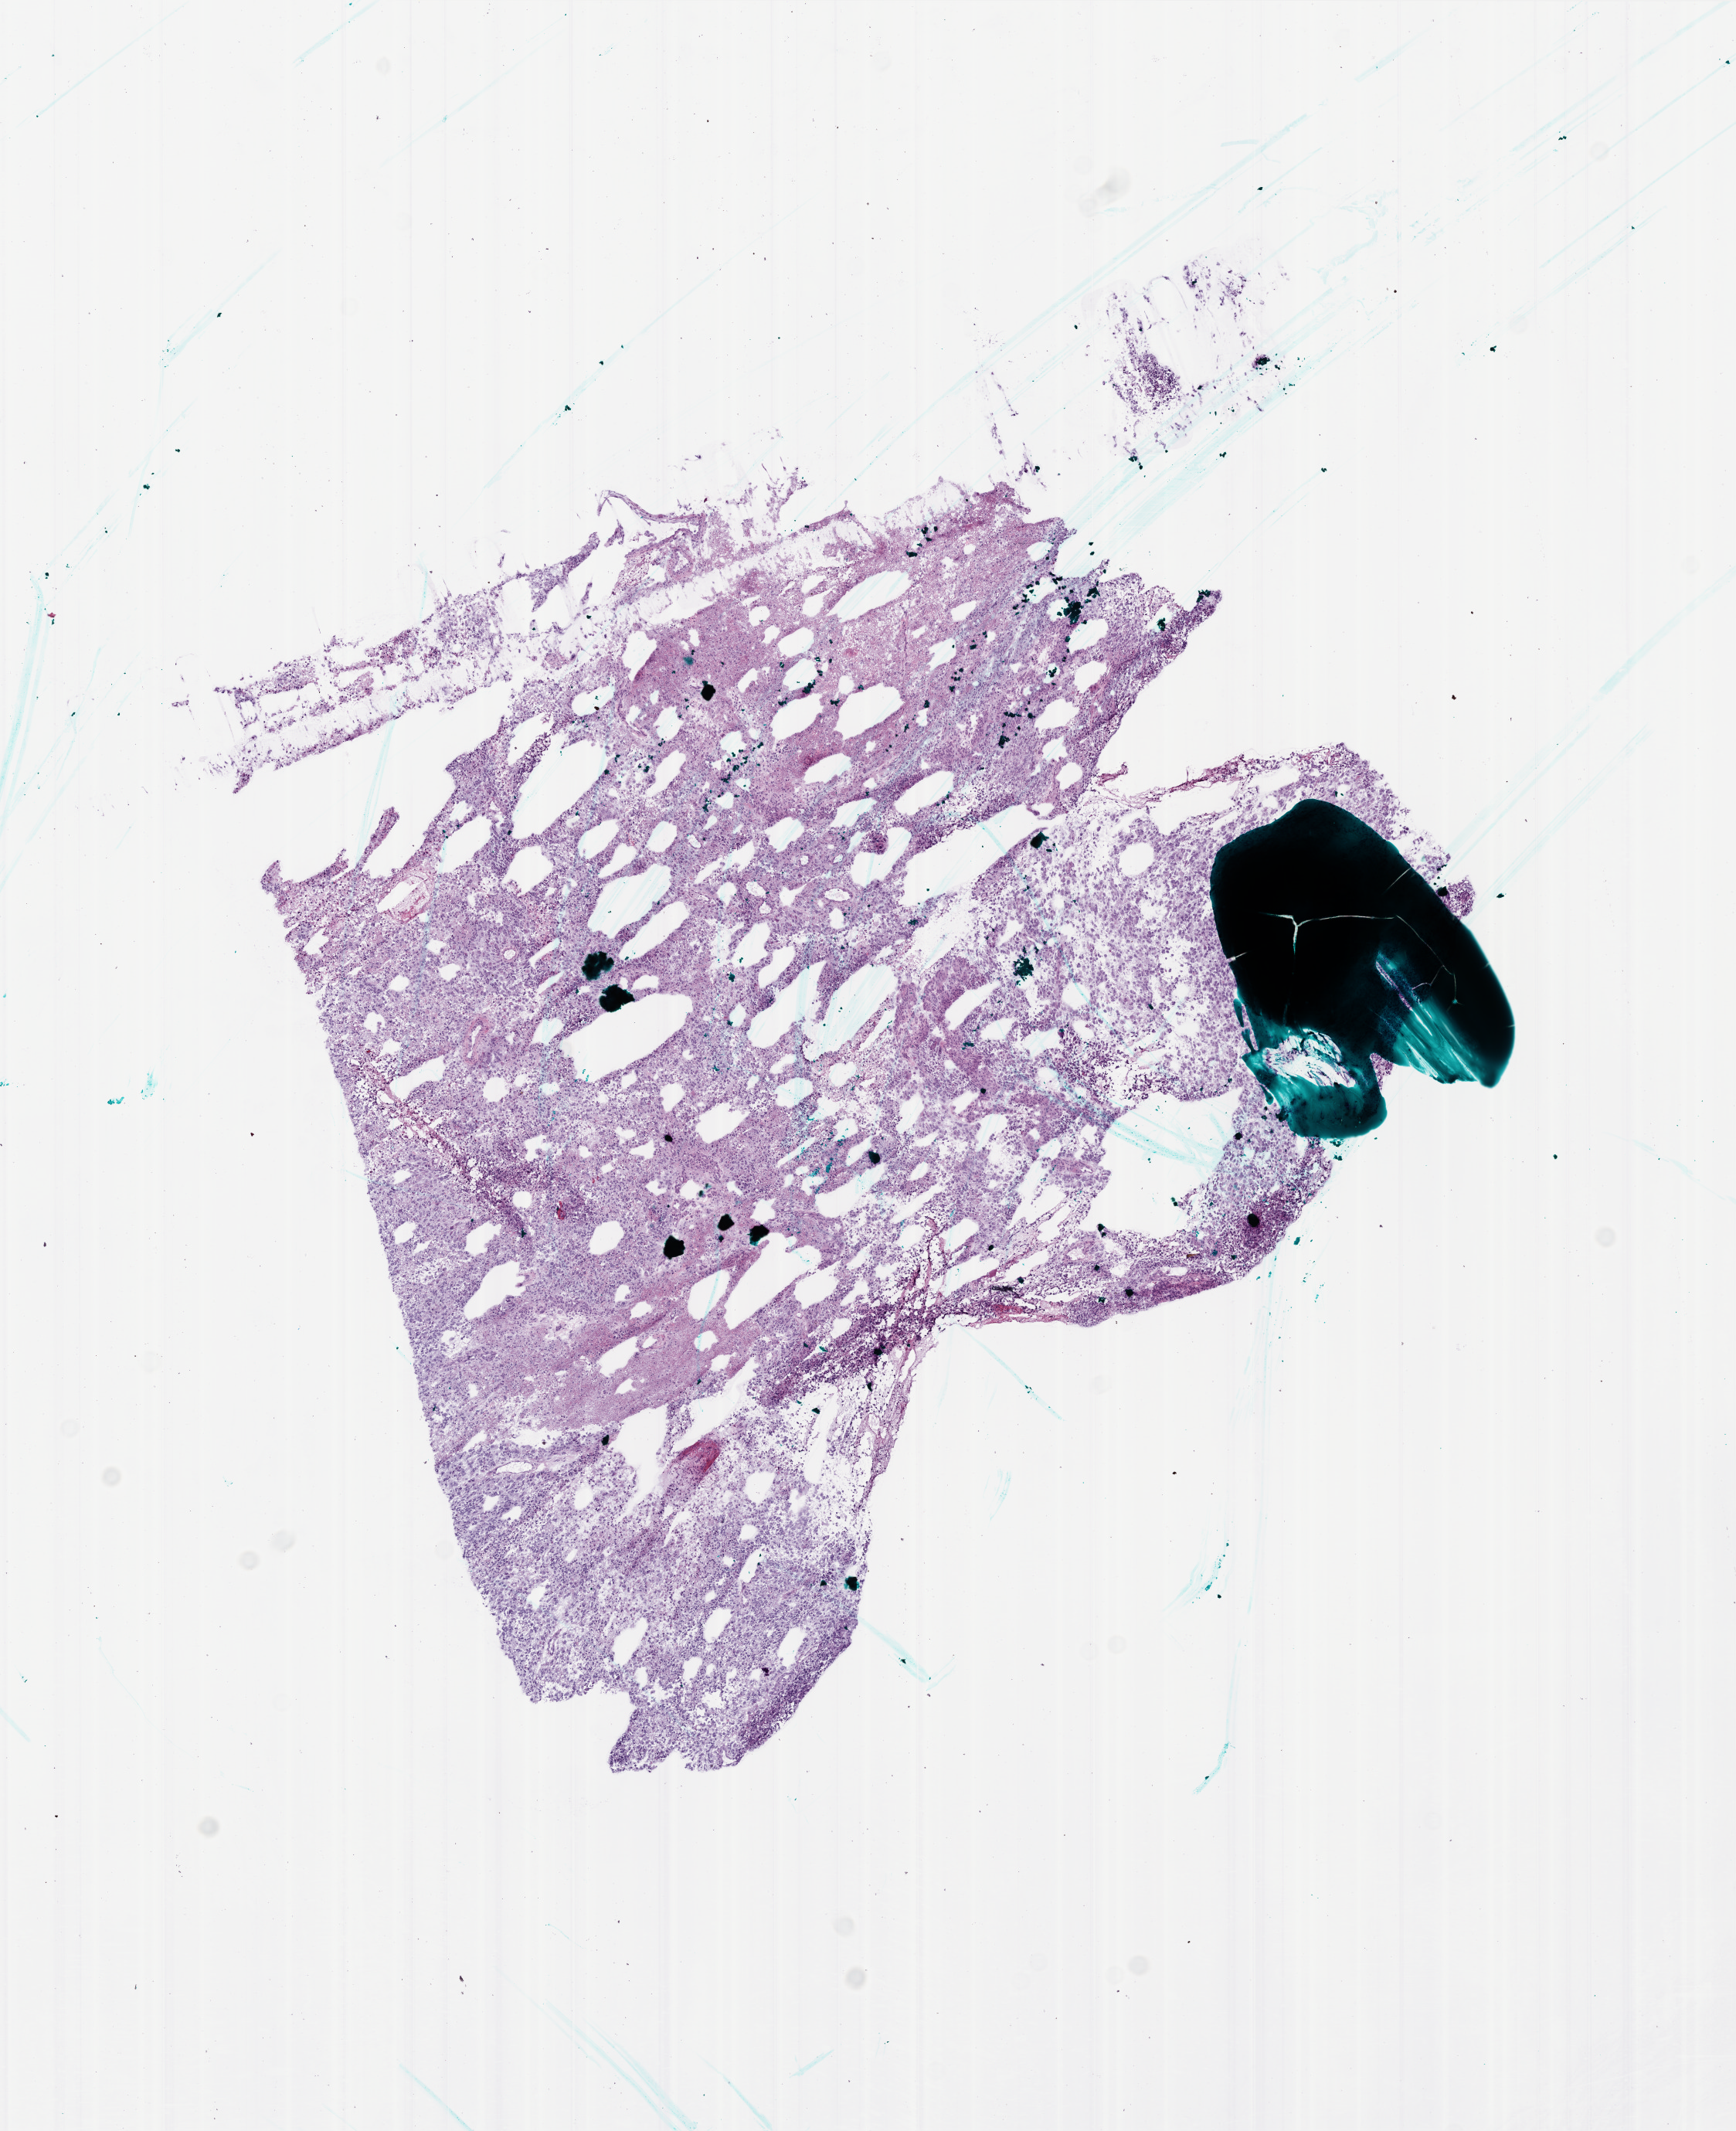
Hematoxylin and eosin (H&E) stained whole-slide image — a low-resolution overview of the entire scanned area, about 9.0 x 11.0 mm (from a 20x scan), frozen section, brain, primary tumour sample. Female patient; age at initial diagnosis 61 years. Composition of this section per pathologist review: tumour cells 95%, tumour nuclei 95%, normal cells 0%, stromal cells 0%, necrosis 5%.
• histologic diagnosis: Glioblastoma